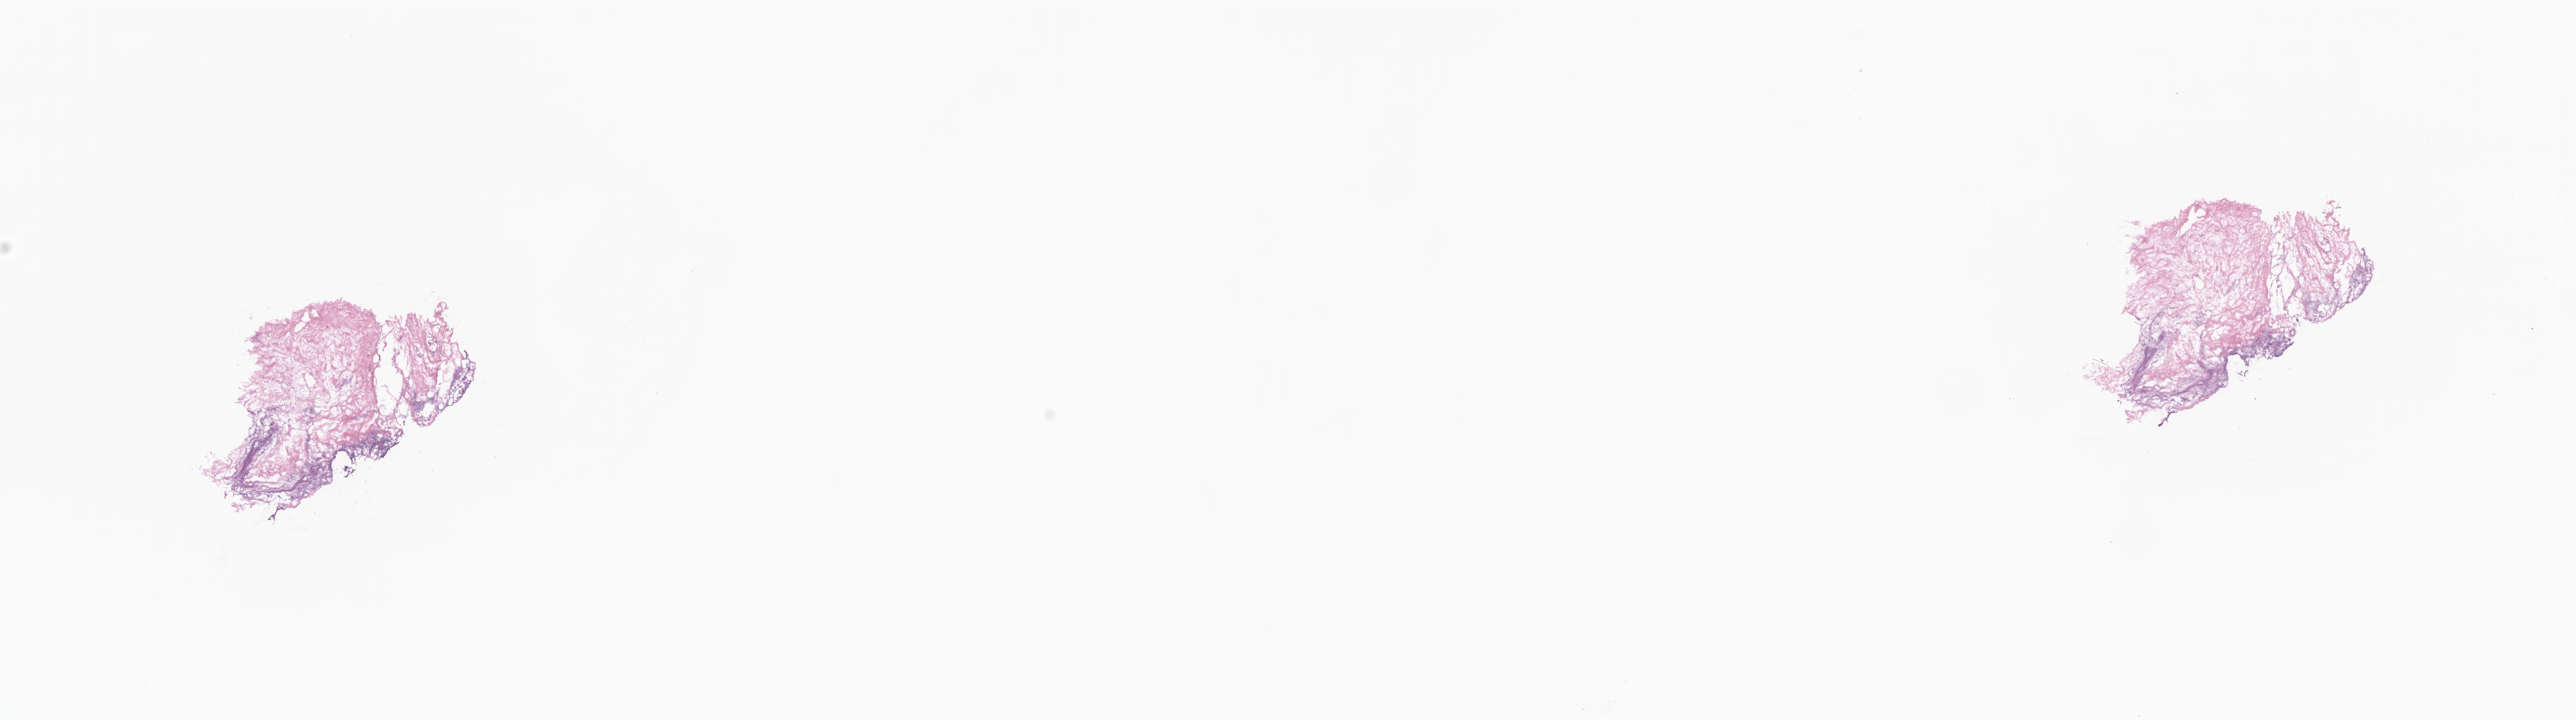
H&E whole-slide image, whole scanned area (about 24.0 x 6.7 mm) shown as a low-resolution overview; cryosection; specimen: primary tumor; site: breast. Patient: female, age at initial diagnosis 64 years. Pathologist review of this section (percent, as recorded): tumor cells 5%, tumor nuclei 40%, stromal cells 90%, necrosis 0%, normal cells 5%. Inflammatory infiltration, as recorded: lymphocyte infiltration 0%, monocyte infiltration 0%, neutrophil infiltration 0%.
Section: top of the tissue portion. Diagnosis: Lobular carcinoma, NOS.